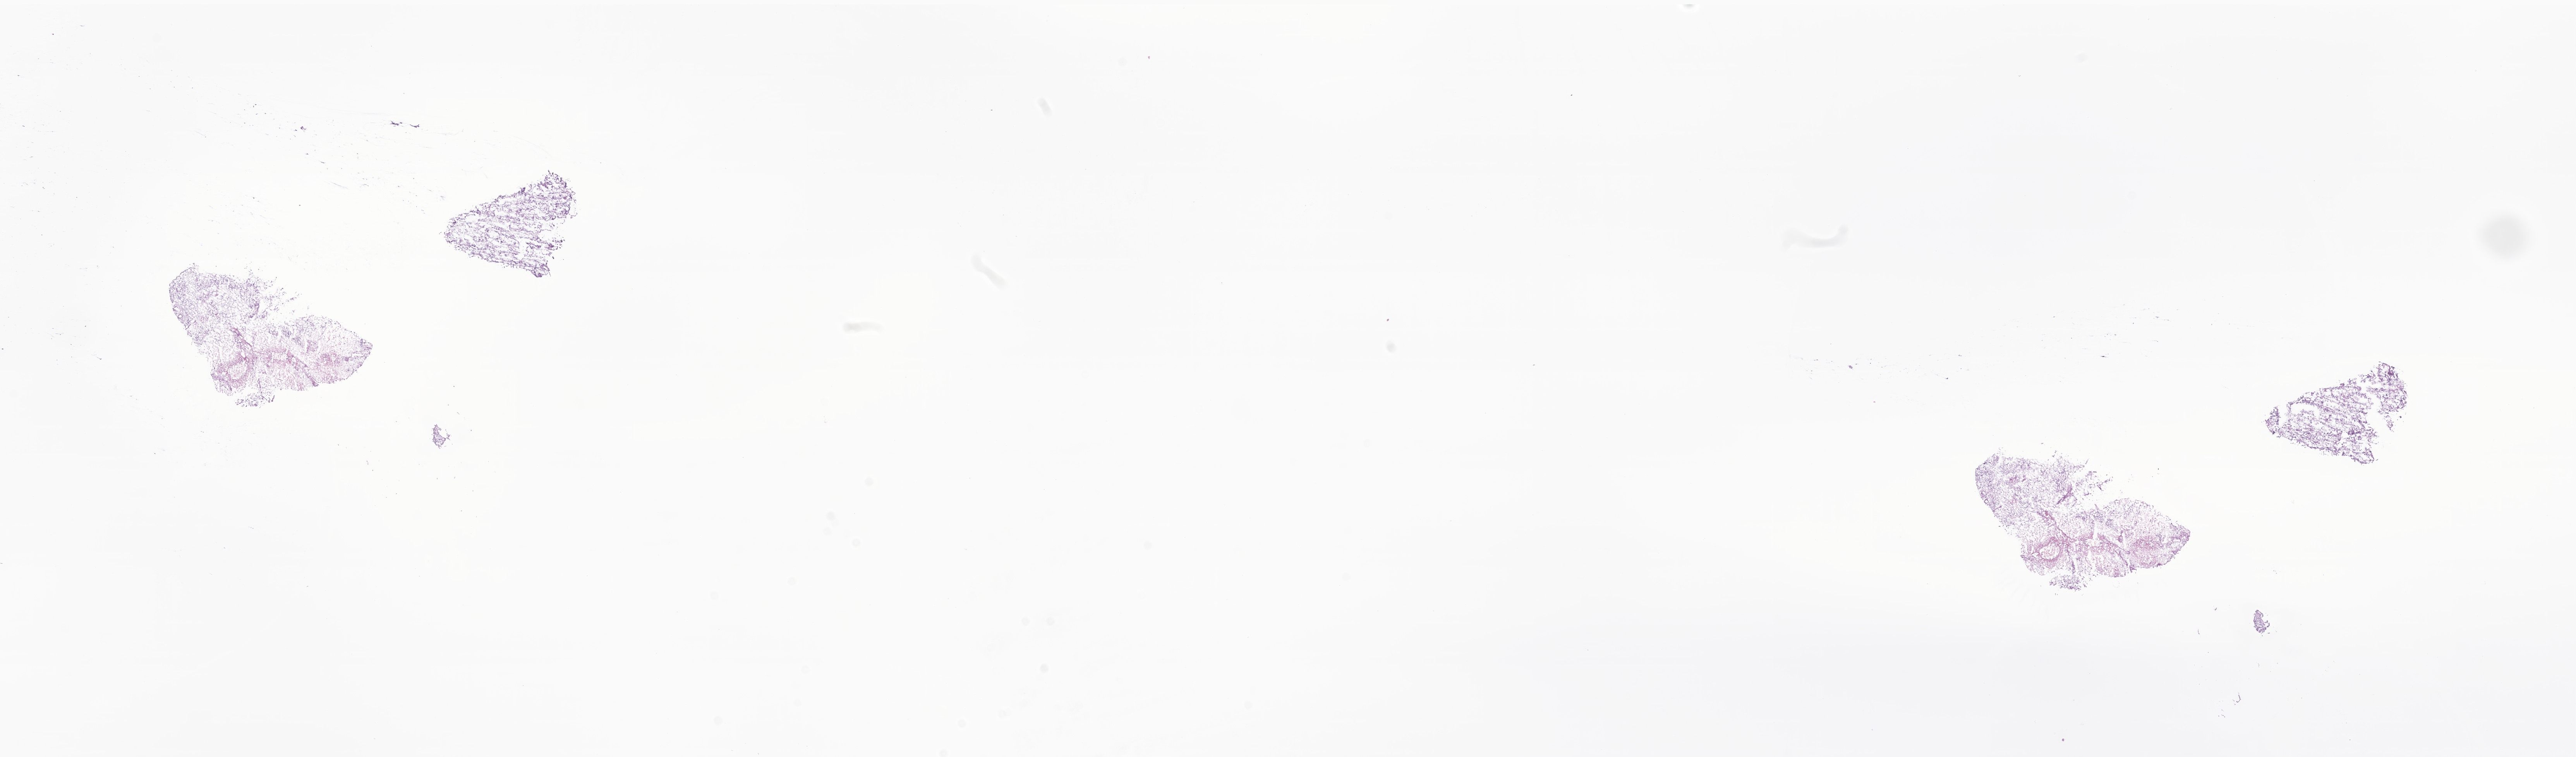
Whole-slide image, haematoxylin and eosin stain of tumor tissue from the brain — low-resolution overview of the scanned area, about 28.0 x 8.2 mm. Cryosection (OCT / tissue freezing medium). Patient: female, age 209 months (17 years 5 months).
Diagnosis: Neoplasm, uncertain whether benign or malignant.